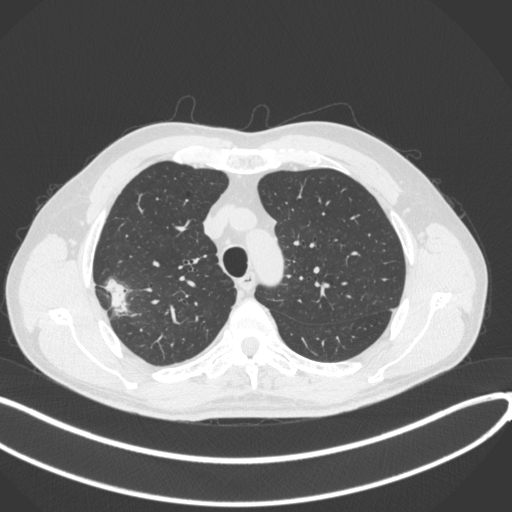
Chest CT, one axial slice. Slice 321 of 381 in the series (ordered by position). Reconstruction kernel B31f. 120 kVp. Lung window (W 1500 / L -600 HU). 1 mm slice thickness. 512 × 512 image matrix. Male patient, age 62 years. From the clinical record (not read from this slice): clinical TNM (as recorded): T1c N0 M0.
Annotated regions visible in this slice (bounding box drawn by a radiologist):
- lung tumour (recorded histology: adenocarcinoma): bounding box (x1, y1, x2, y2) in pixels: (99, 270, 133, 321)